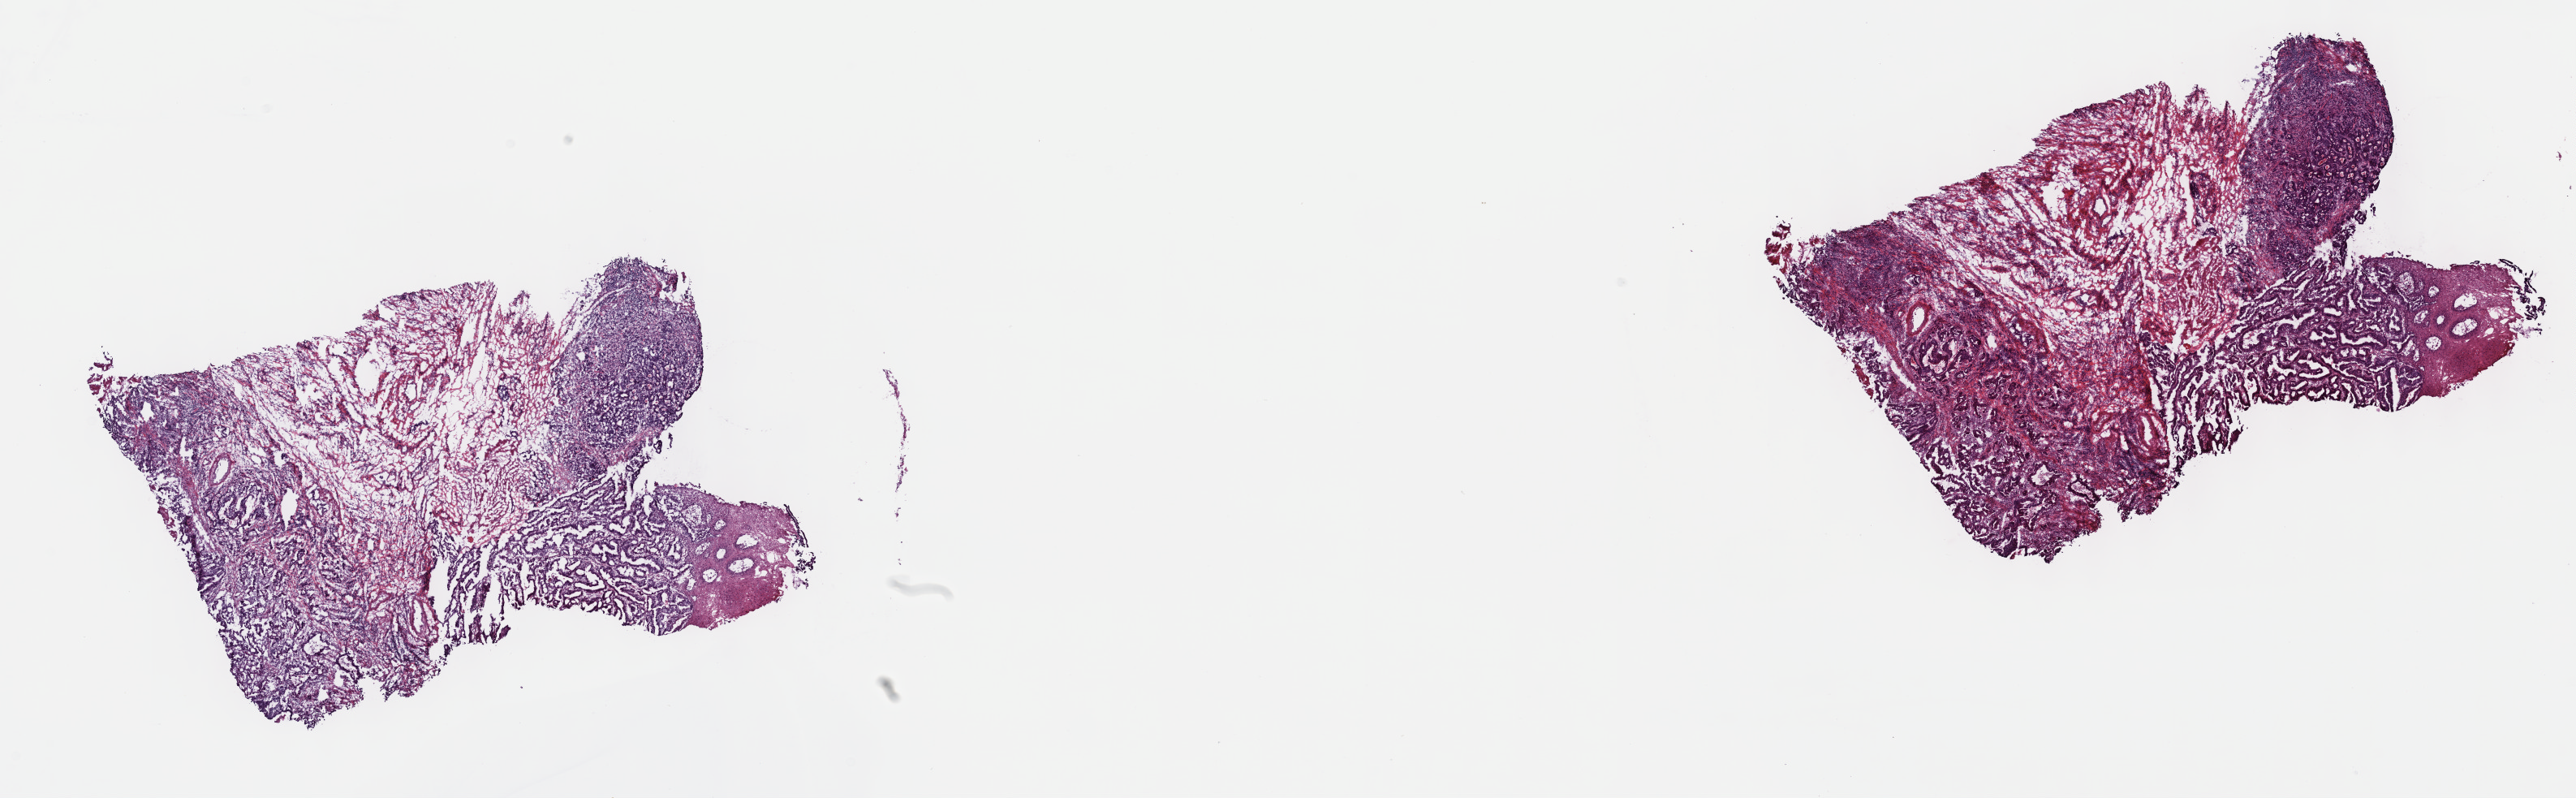
H&E-stained whole-slide image, whole scanned area (about 25.7 x 8.0 mm) shown as a low-resolution overview. Frozen section from the top of the tissue portion. Primary tumour sample from the stomach. Male patient; age at initial diagnosis 59 years.
Pathologic diagnosis: Tubular adenocarcinoma.